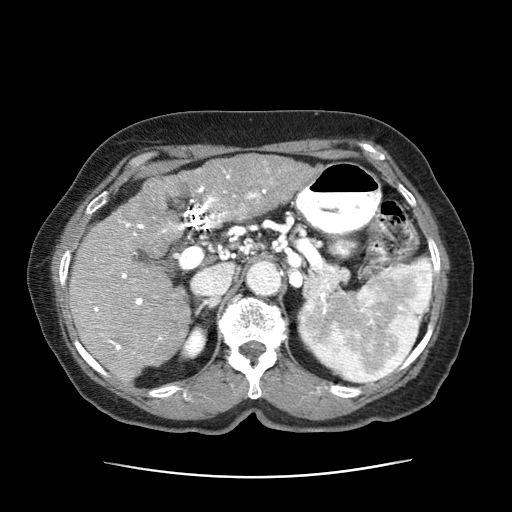
Contrast-enhanced abdominal CT (liver protocol), one axial slice. Slice 35 of 63 in the series (ordered by position). Reconstruction kernel STANDARD. 120 kVp. Intravenous contrast given. Soft-tissue window (W 400 / L 40 HU). 2.5 mm slice thickness. 512 × 512 image matrix, field of view 360 × 360 mm. Patient: female, 79 years. From the clinical record (not read from this slice): diagnosis: hepatocellular carcinoma (patient treated with transarterial chemoembolisation; whether this scan precedes or follows treatment is not stated here); TNM stage (as recorded): Stage-II; Child-Pugh class: B; tumour differentiation: well differentiated; tumour nodularity: multinodular.
Annotated regions visible in this slice (semi-automatic segmentation, software-assisted and operator-edited):
- abdominal aorta: box from (x=246, y=261) to (x=282, y=296) px
- liver parenchyma outside the tumour (the mass and vessels are separate outlines, so this box may not span the whole liver): (x=67, y=177)–(x=192, y=381)
- mass: (x=159, y=153)–(x=314, y=218)
- liver vessels: (x=88, y=174)–(x=267, y=354)